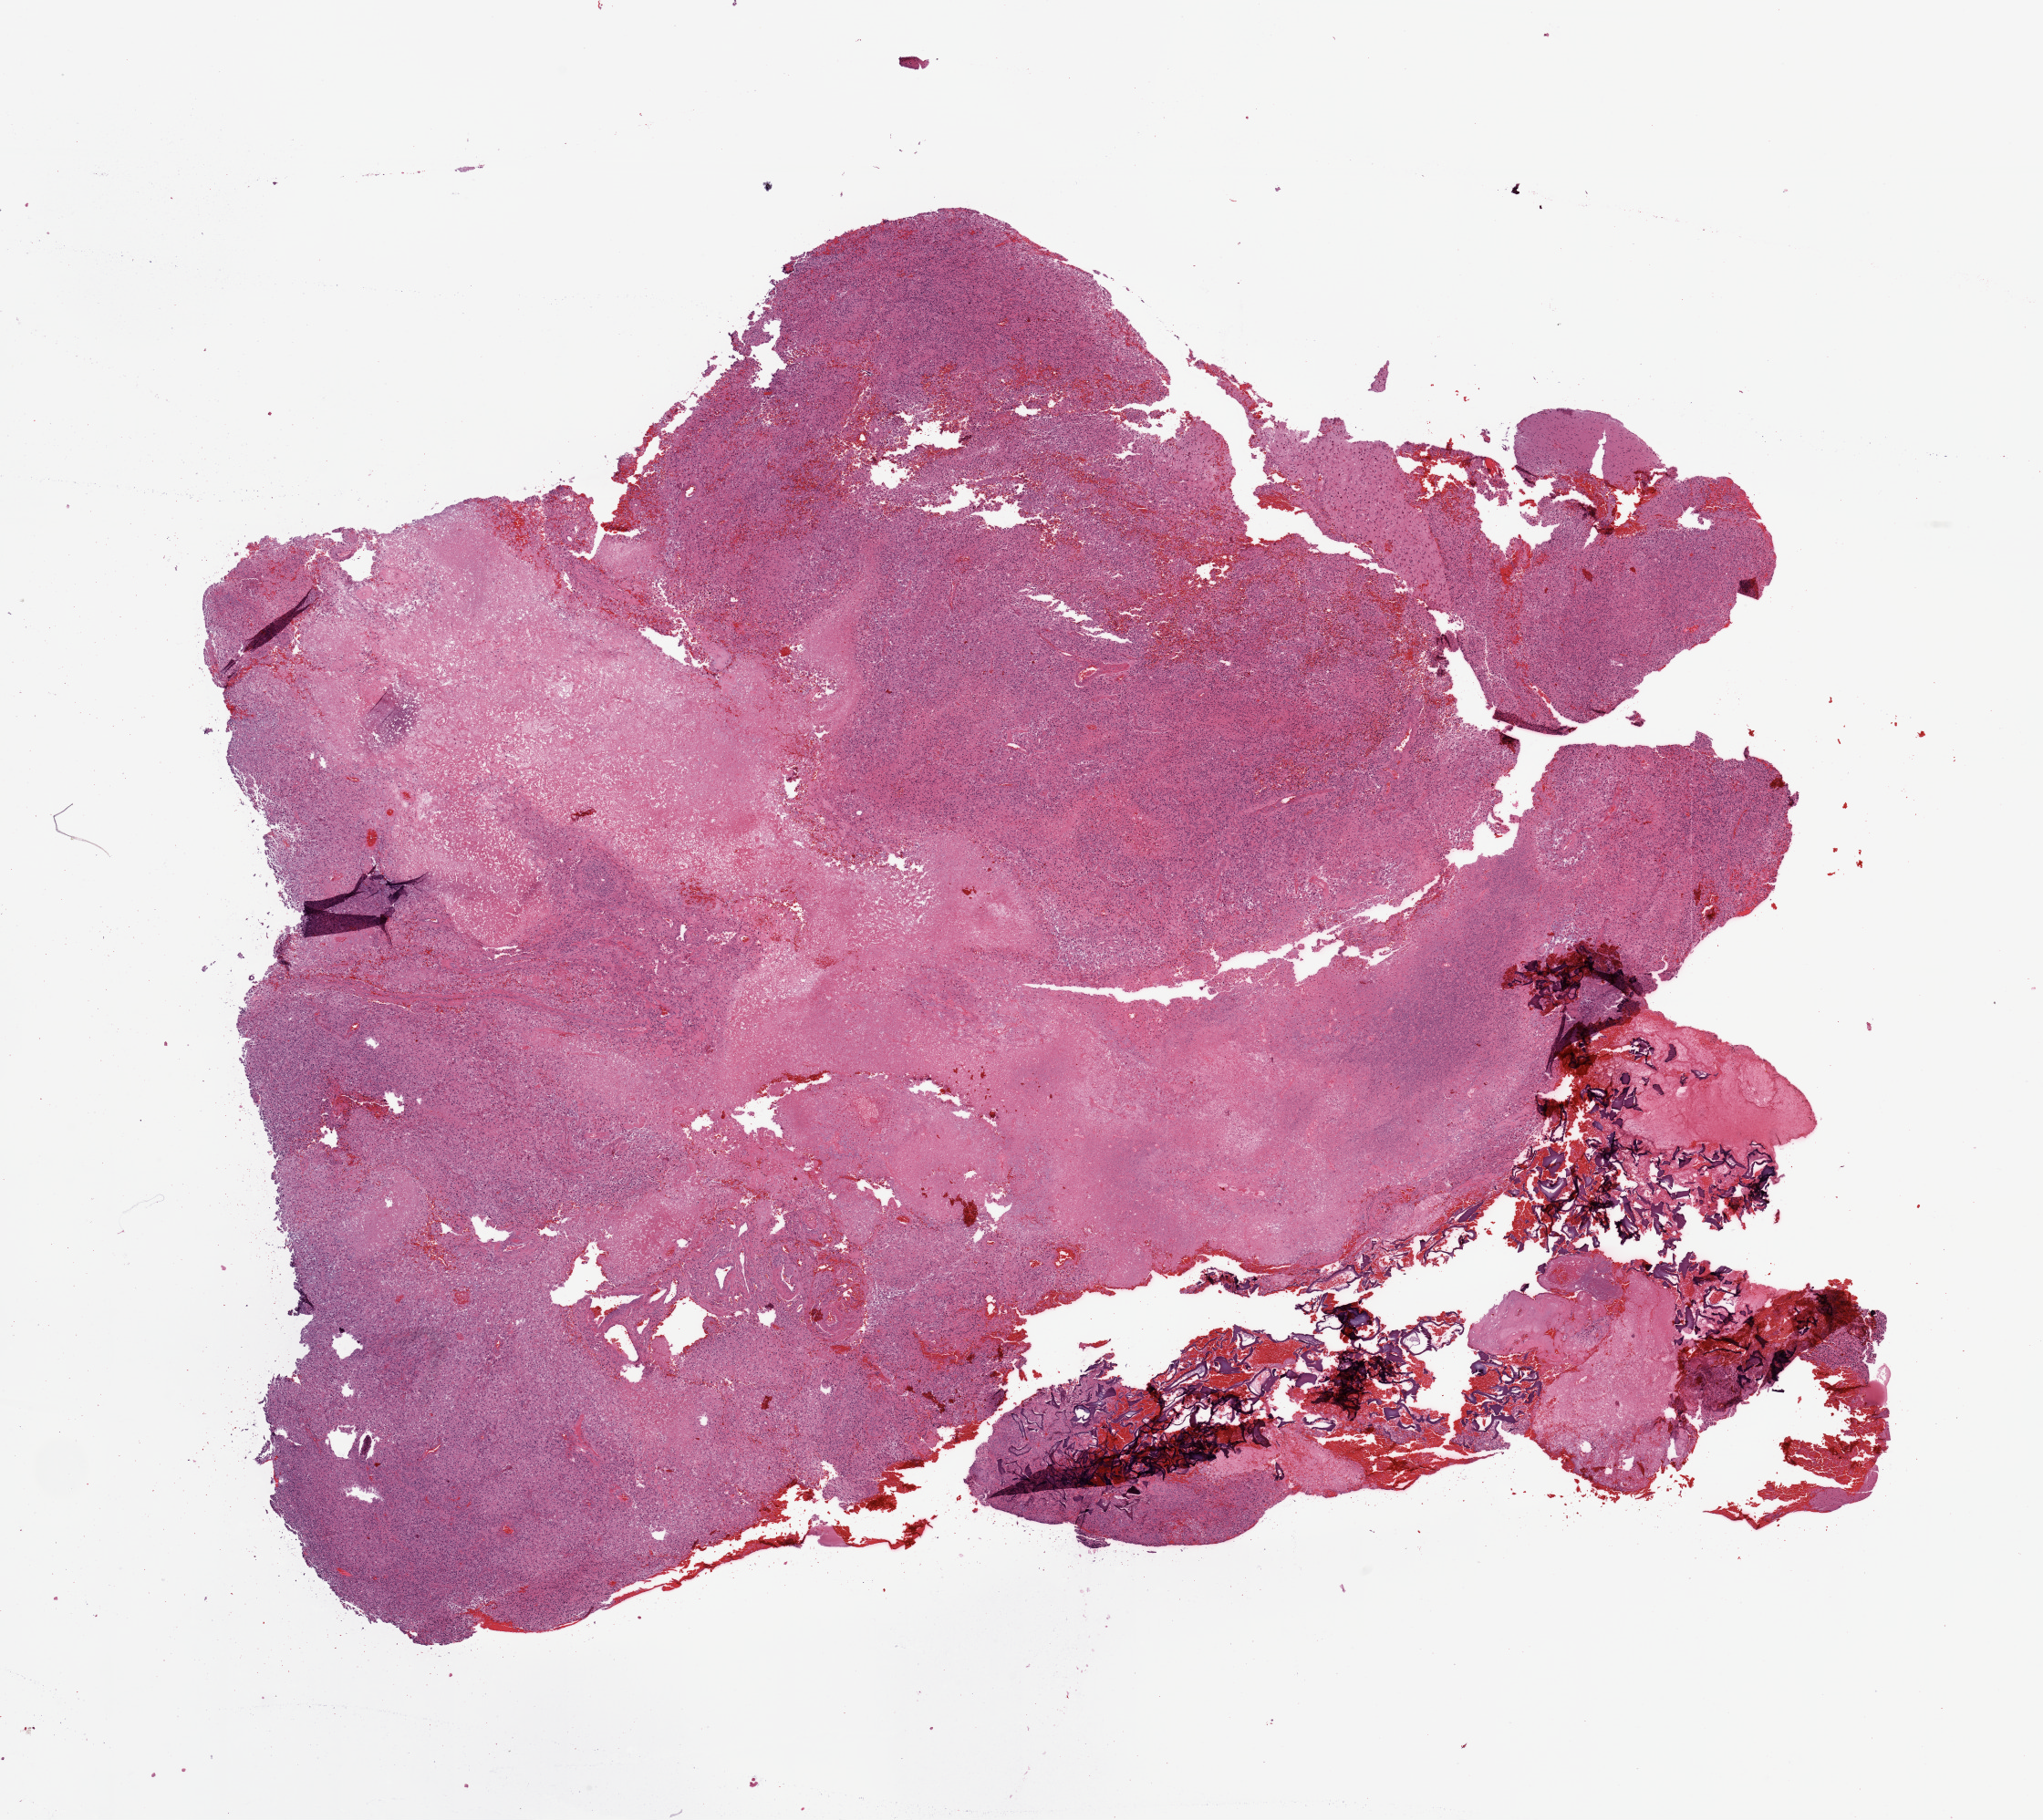
Hematoxylin and eosin (H&E) stained whole-slide image — whole scanned area (about 17.7 x 15.8 mm, from a 20x scan) shown as a low-resolution overview. Tumour tissue sample, sampled site: frontal lobe. 60-year-old male patient. Slide review estimates, as recorded: tumour nuclei 65%, necrosis 35%.
- primary tumour site (as recorded): frontal lobe
- histologic diagnosis: Glioblastoma